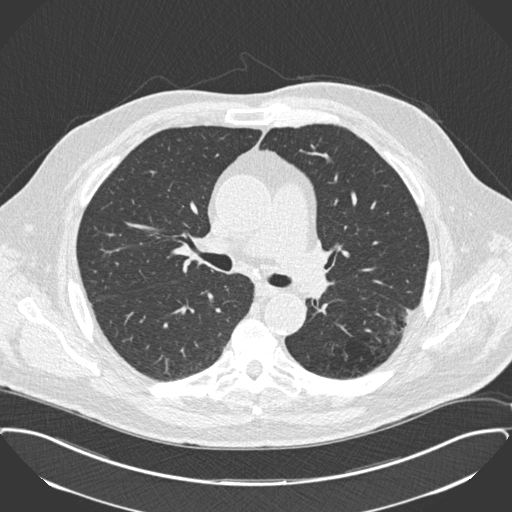
Low-dose screening chest CT, one axial slice; position 105 of 175 along the scan axis; 120 kVp; lung window (W 1500 / L -600 HU); 2 mm slice thickness; 512 × 512 image matrix, field of view 400 × 400 mm.
Annotated regions visible in this slice (outlined manually by an expert reader):
- lesion 1 (tumor, lower lobe of left lung): bounding box (x1, y1, x2, y2) in pixels: (406, 309, 410, 314)